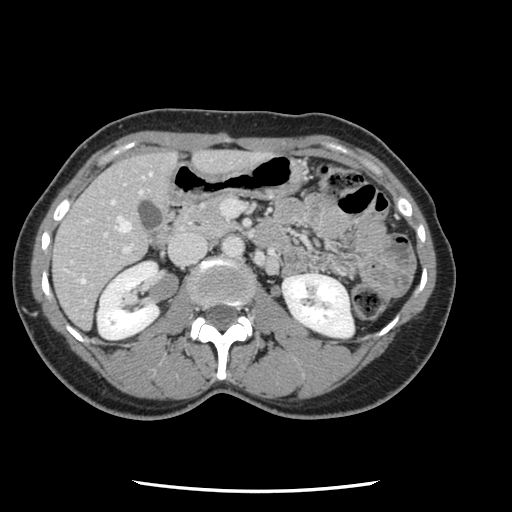
Contrast-enhanced abdominal CT, one axial slice; intravenous contrast given; soft-tissue window (W 400 / L 40 HU); 2.5 mm slice thickness; 512 × 512 image matrix, field of view 330 × 330 mm. Female patient, age 43 years. From the clinical record (not read from this slice): diagnosis: colorectal cancer liver metastases, imaged before liver resection; multiple liver metastases: yes; largest metastasis: 3.4 cm; disease in both lobes: yes.
Structures marked on this image (expert manual segmentation):
- hepatic veins: box from (x=81, y=173) to (x=151, y=283) px
- liver: (x=54, y=153)–(x=257, y=327)
- planned liver remnant (the part of the liver to remain after resection): (x=54, y=153)–(x=176, y=327)
- portal vein (with intrahepatic branches): (x=70, y=201)–(x=243, y=303)